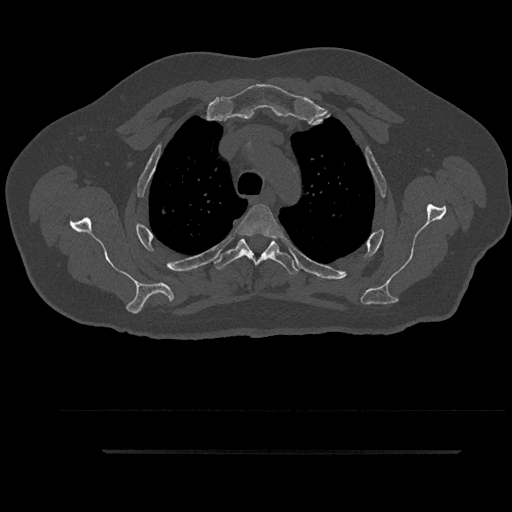
CT including the spine, one axial slice. Position 694 of 797 along the scan axis. Bone window (W 1800 / L 400 HU). 0.5 mm slice thickness. 512 × 512 image matrix. Patient: male, 63 years. From the clinical record (not read from this slice): primary cancer: renal.
Structures marked on this image (semi-automatic segmentation, software-assisted and operator-edited):
- T3 vertebra: box from (x=237, y=204) to (x=282, y=238) px
- T4 vertebra: (x=212, y=236)–(x=300, y=274)